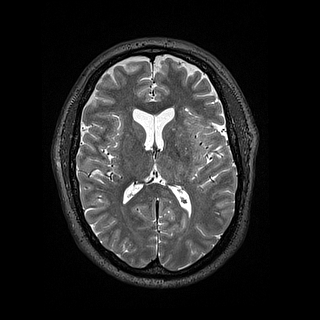
Brain MRI from a brain-tumour surgery series, one axial slice. Slice 77 of 144 in the series (ordered by position). 1.2 mm slice thickness. 320 × 320 image matrix. Case-level facts recorded for this patient, not image findings: histopathology: Astrocytoma; WHO grade: 2; IDH mutation: yes.
Outlined on this slice (manually delineated by an expert):
- tumour: bounding box <190,146,208,176> (left, top, right, bottom; pixels)